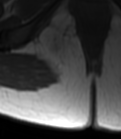
MRI of an extremity soft-tissue mass, one axial slice; slice 32 of 47 in the series (ordered by position); MR volume resampled by the dataset authors to the PET/CT grid (not the native acquisition matrix); 3.27 mm slice thickness; 121 × 139 image matrix. Female patient. From the clinical record (not read from this slice): histological type: epithelioid sarcoma; grade: intermediate; site of the primary tumour: right buttock.
Annotated regions visible in this slice (expert contour drawn on MRI and transferred to this co-registered scan by the dataset authors):
- gross tumour volume including surrounding oedema: bounding box (x1, y1, x2, y2) in pixels: (41, 25, 76, 67)
- gross tumour volume (mass): (43, 32, 67, 58)